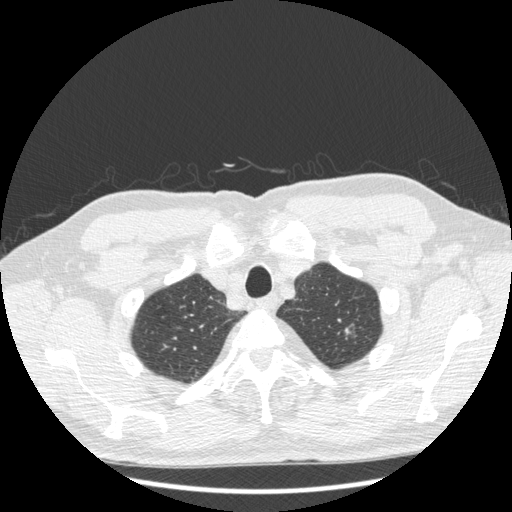
Low-dose screening chest CT, one axial slice. 120 kVp. Lung window (W 1500 / L -600 HU). 1.25 mm slice thickness. 512 × 512 image matrix, field of view 380 × 380 mm.
Structures marked on this image (expert manual segmentation):
- lesion 1 (tumor, upper lobe of left lung): bounding box <344,325,354,340> (left, top, right, bottom; pixels)